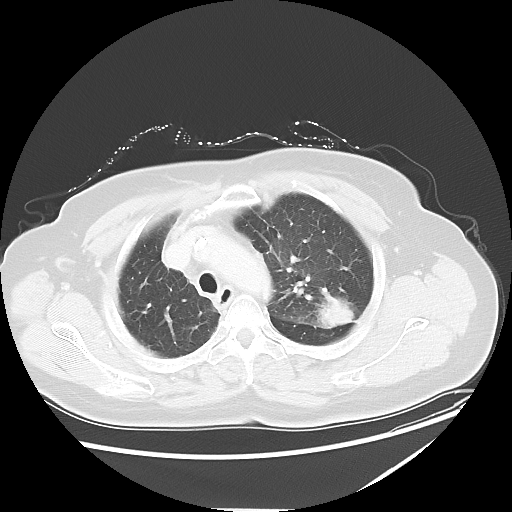
Chest CT, one axial slice. Position 42 of 54 along the scan axis. Reconstruction kernel LUNG. 120 kVp. Lung window (W 1500 / L -600 HU). 512 × 512 image matrix. Female patient, age 61 years. Case-level facts recorded for this patient, not image findings: clinical TNM (as recorded): T1c N3 M1.
Outlined on this slice (bounding box drawn by a radiologist):
- lung tumour (recorded histology: adenocarcinoma): box from (x=305, y=286) to (x=359, y=331) px